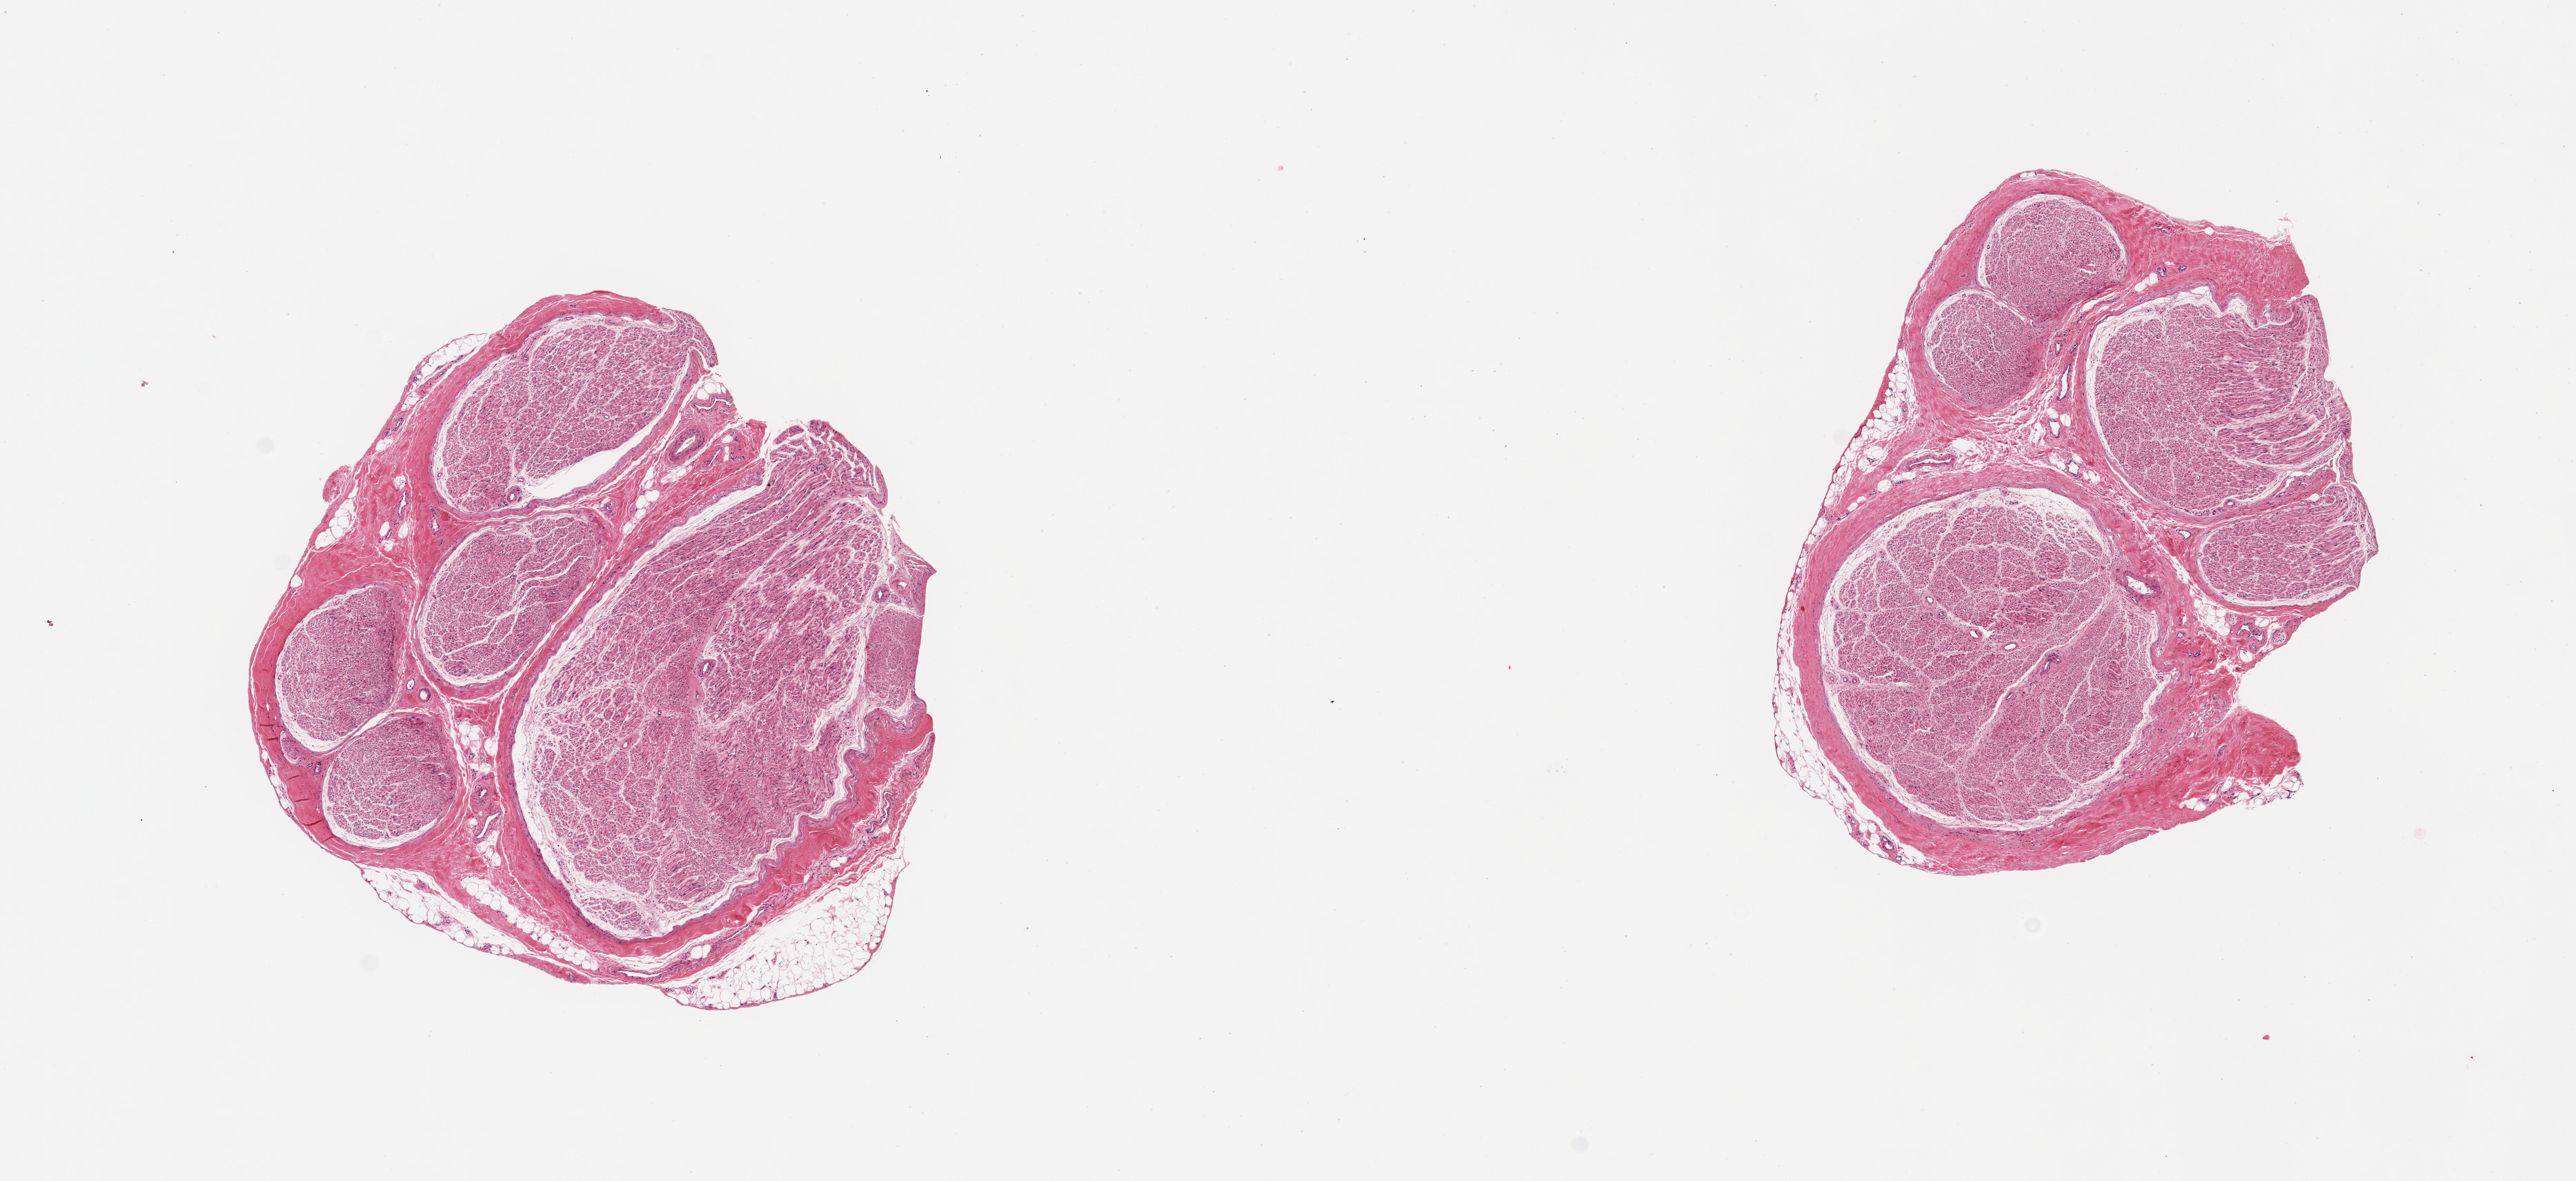
Digitized H&E-stained section — shown as a low-resolution overview of the whole scanned area (about 14.8 x 6.8 mm, from a 20x scan), PAXgene-fixed, paraffin-embedded tissue, target tissue: tibial nerve, donor tissue sample. Donor: male.
• reviewer comment on this tissue sample: 2 pieces; minimal partial rim of adipose tissue